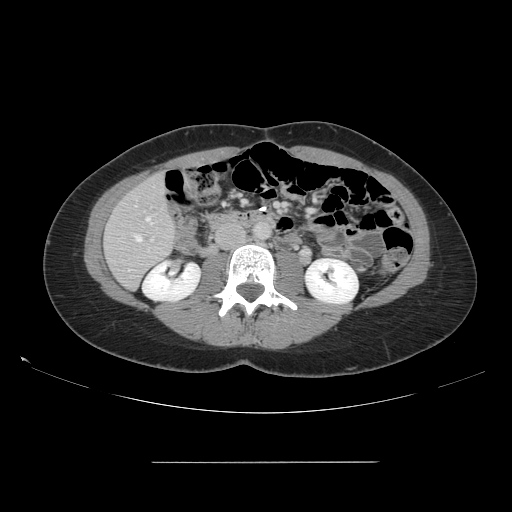
Contrast-enhanced abdominal CT, one axial slice. Position 48 of 151 along the scan axis. 120 kVp. Intravenous contrast given. Soft-tissue window (W 400 / L 40 HU). 2.5 mm slice thickness. 512 × 512 image matrix, field of view 421 × 421 mm. Female patient, age 46 years. From the clinical record (not read from this slice): diagnosis: colorectal cancer liver metastases, imaged before liver resection; multiple liver metastases: yes; largest metastasis: 3 cm; chemotherapy before resection: no.
Outlined on this slice (outlined manually by an expert reader):
- hepatic veins: bounding box (x1, y1, x2, y2) in pixels: (135, 217, 151, 241)
- liver: (105, 175, 176, 289)
- planned liver remnant (the part of the liver to remain after resection): (105, 175, 175, 288)